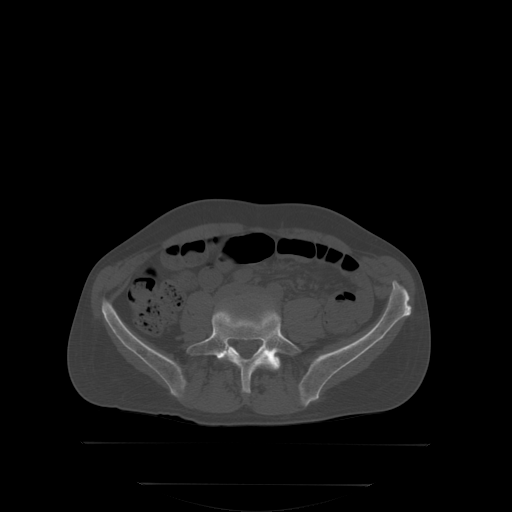
CT including the spine, one axial slice. Slice 97 of 350 in the series (ordered by position). Bone window (W 1800 / L 400 HU). 512 × 512 image matrix. Male patient, age 58 years. Case-level facts recorded for this patient, not image findings: primary cancer: prostate.
Annotated regions visible in this slice (semi-automatic segmentation, software-assisted and operator-edited):
- L4 vertebra: bounding box [x1, y1, x2, y2] px = [261, 354, 268, 362]
- L5 vertebra: [188, 307, 299, 392]